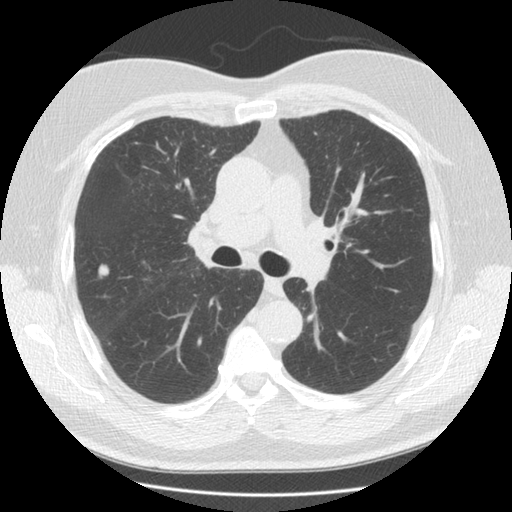
Low-dose screening chest CT, one axial slice; slice 88 of 146 in the series (ordered by position); reconstruction kernel STANDARD; 120 kVp; lung window (W 1500 / L -600 HU); 2.5 mm slice thickness; 512 × 512 image matrix.
Structures marked on this image (manually delineated by an expert):
- lesion 1 (tumor, upper lobe of right lung): bounding box <97,263,110,279> (left, top, right, bottom; pixels)